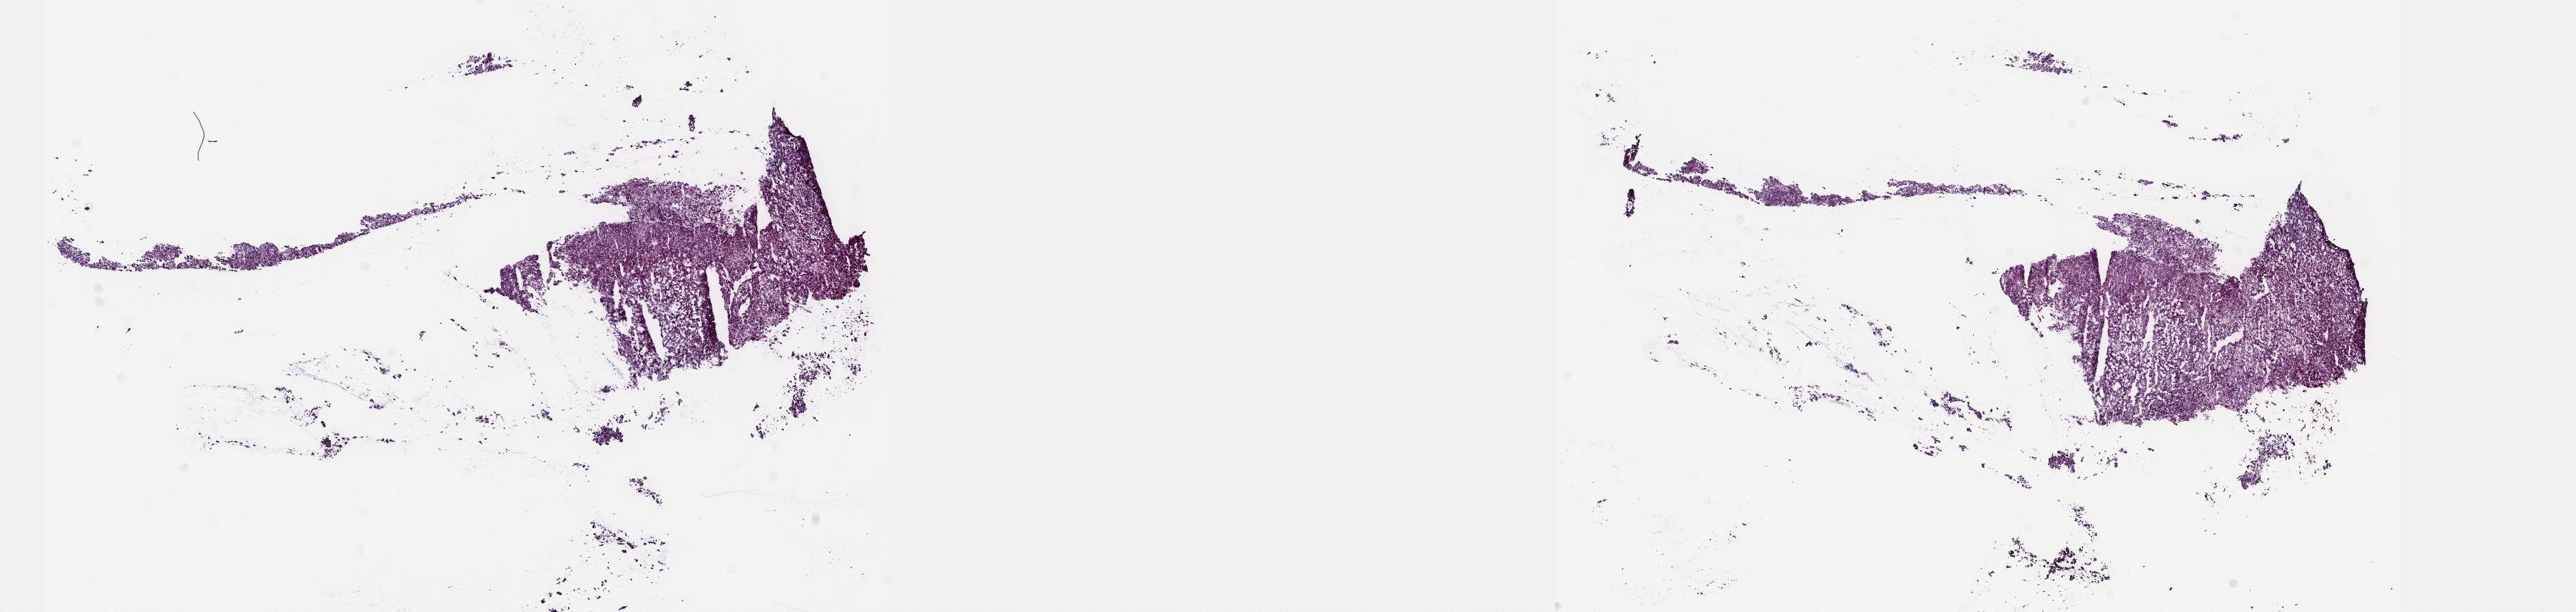
Digitized H&E-stained tissue section (whole slide) — whole scanned area (about 29.2 x 6.9 mm, acquisition: 40x scan) shown as a low-resolution overview. Frozen section from the top of the tissue portion. Sample: primary tumour, liver. Male, age 70 years at initial diagnosis. Histologic grade: G3 (poorly differentiated). Pathologist review of this section (percent, as recorded): tumour cells 80%, tumour nuclei 80%, normal cells 0%, stromal cells 20%, necrosis 0%. Infiltration values recorded for this section: lymphocyte infiltration 3%, monocyte infiltration 1%, neutrophil infiltration 3%.
Diagnosis: Hepatocellular carcinoma, NOS. AJCC pathologic stage: IIIA.